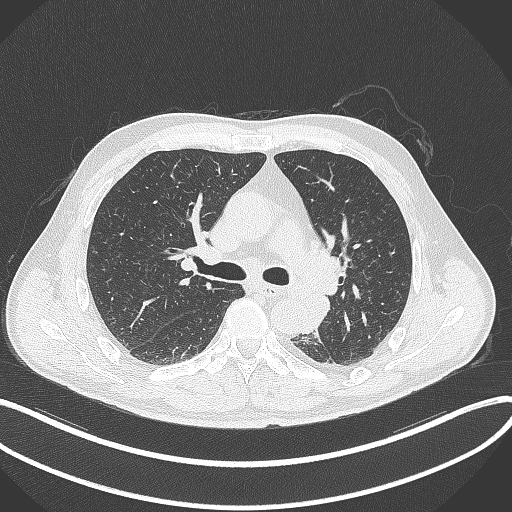
Chest CT, one axial slice. Position 215 of 329 along the scan axis. Reconstruction kernel B70f. 120 kVp. Lung window (W 1500 / L -600 HU). 1 mm slice thickness. 512 × 512 image matrix, field of view 400 × 400 mm. Patient: male, 59 years. From the clinical record (not read from this slice): clinical TNM (as recorded): T2a N2 M0.
Structures marked on this image (rectangle marked by the reading radiologist):
- lung tumour (recorded histology: squamous cell carcinoma): box from (x=301, y=294) to (x=333, y=336) px